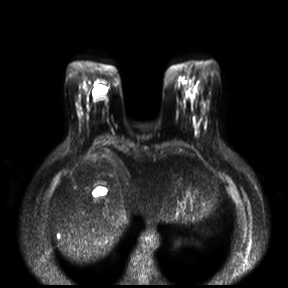
Breast MRI, one axial slice; position 7 of 30 along the scan axis; diffusion-weighted series; image 2 of 4 stored at this slice position (different b-values; order by instance number); 3 T; 4 mm slice thickness; 288 × 288 image matrix, field of view 360 × 360 mm. Female patient.
Structures marked on this image (outlined manually by an expert reader):
- tumour on diffusion-weighted imaging: bounding box (x1, y1, x2, y2) in pixels: (185, 90, 194, 99)